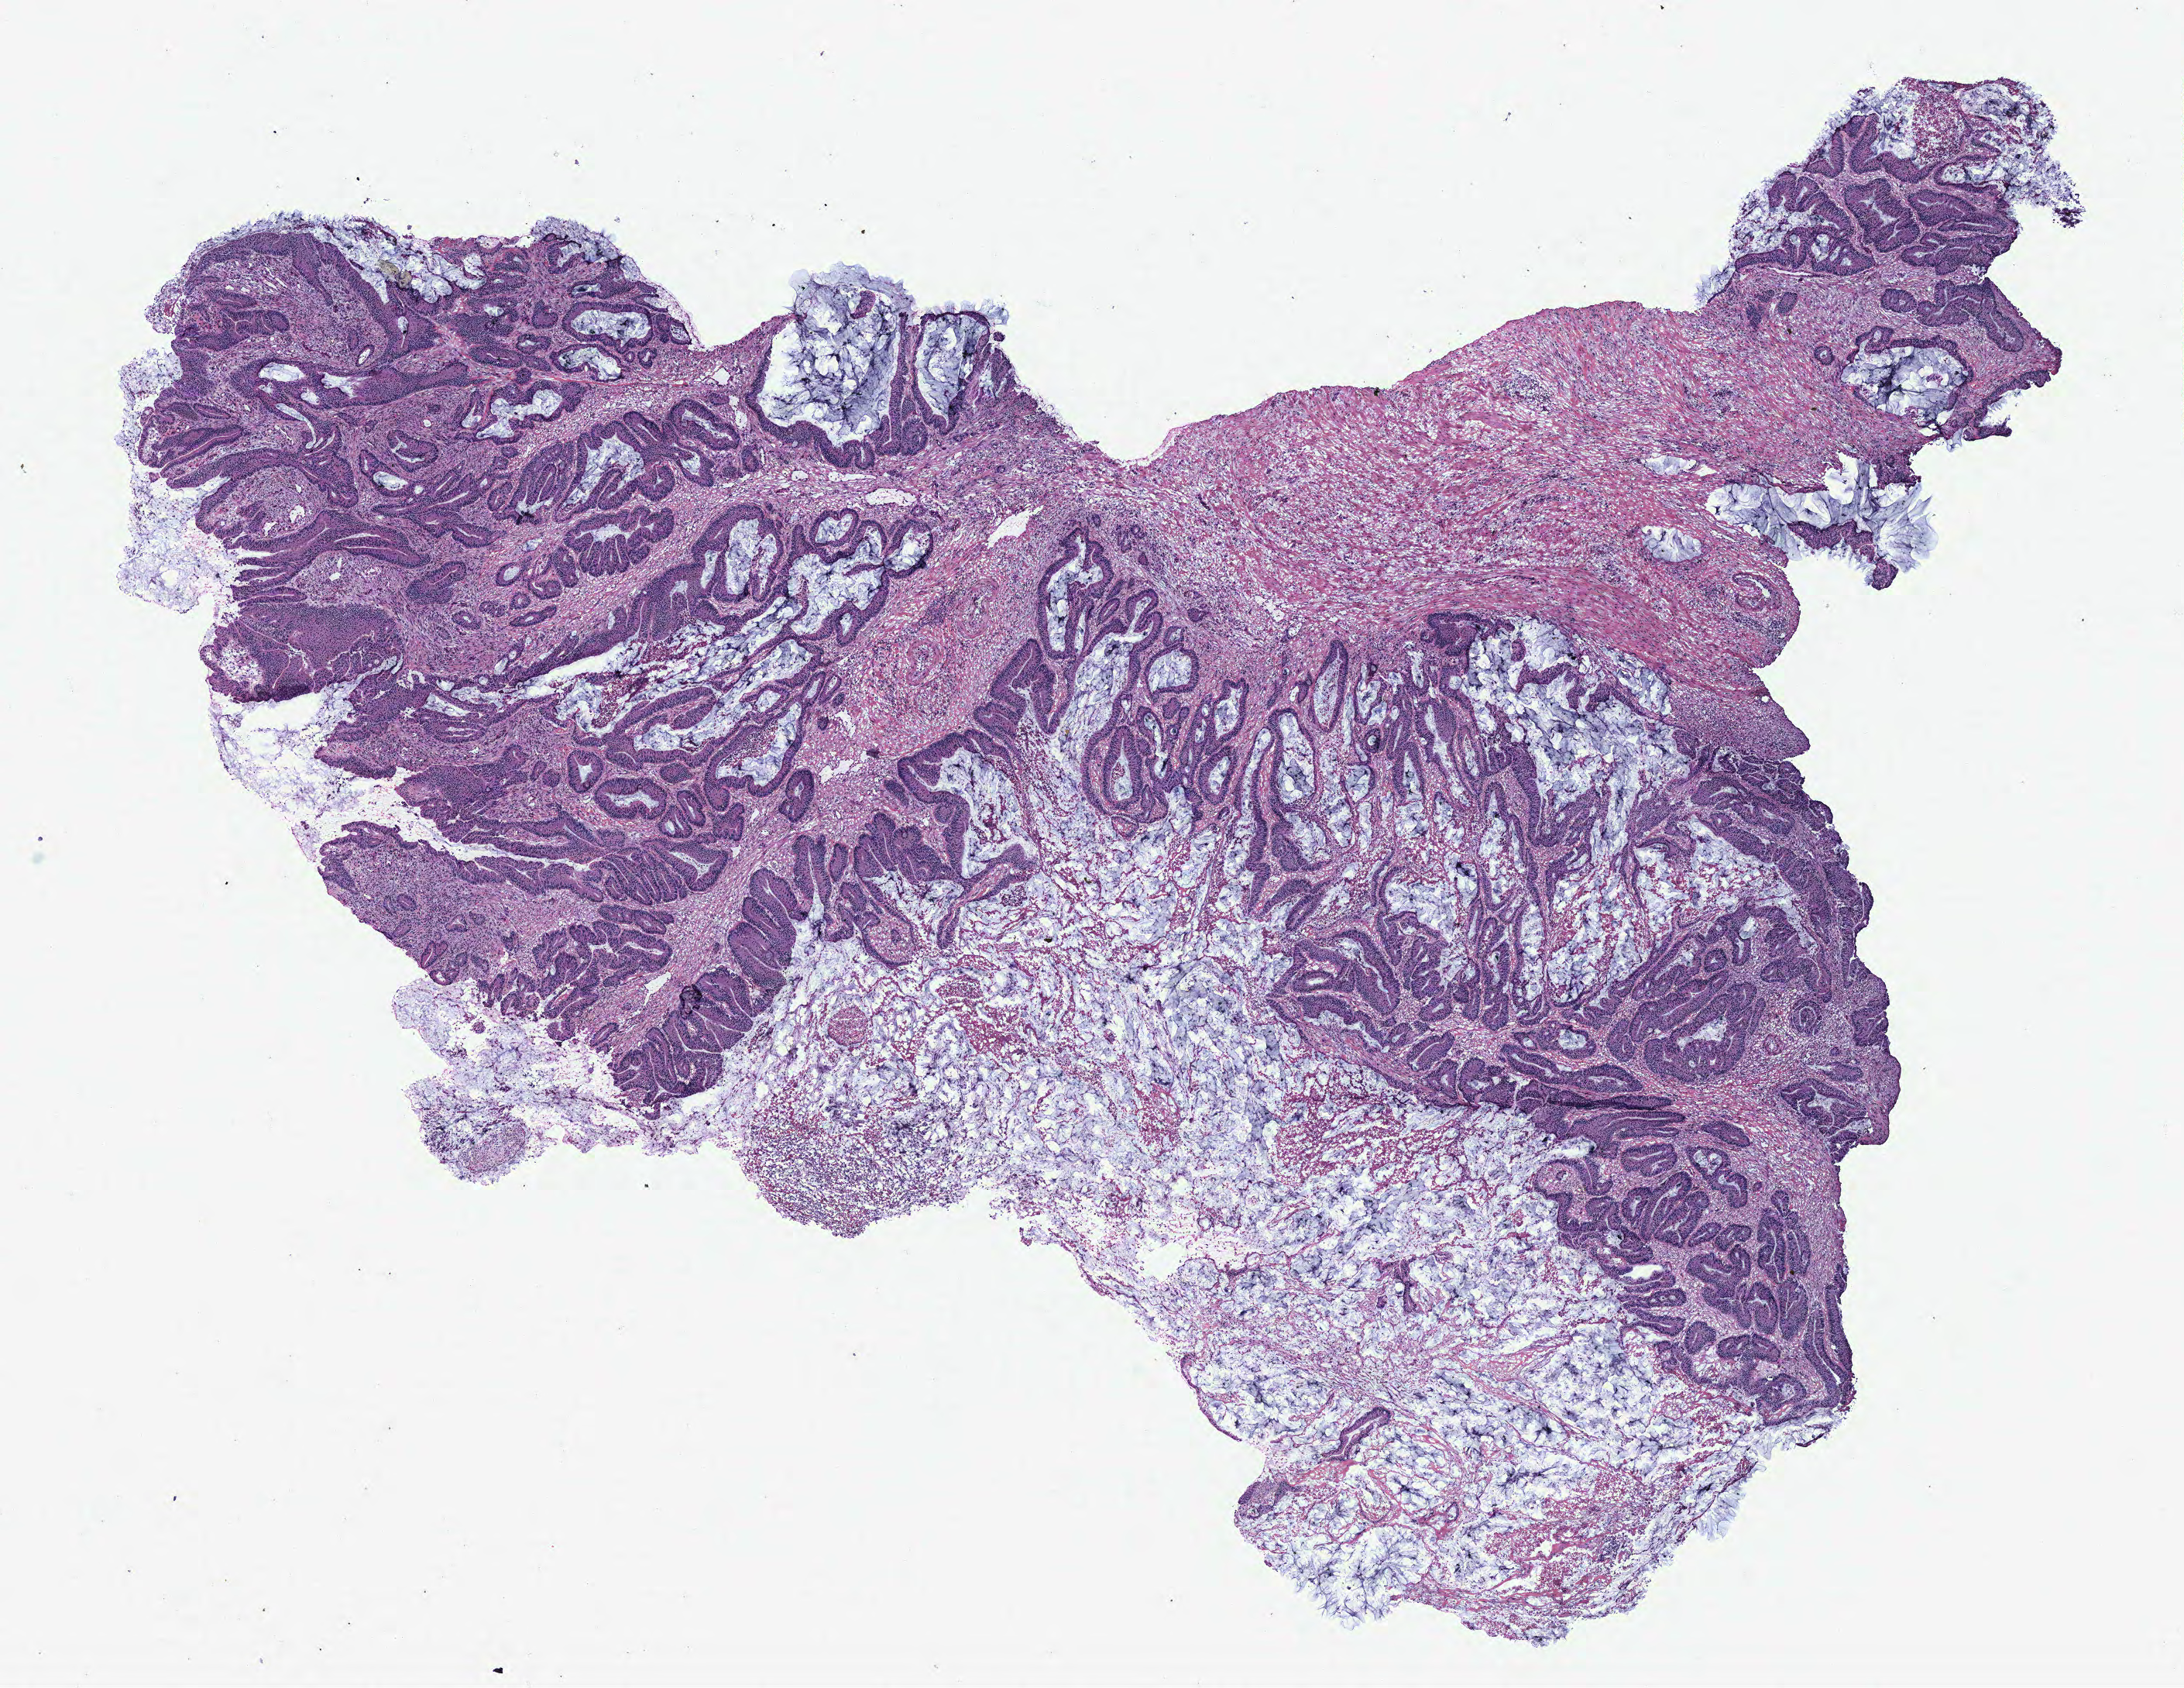
H&E whole-slide image, shown as a low-resolution overview of the whole scanned area (about 11.3 x 8.7 mm, from a 40x scan); tumour tissue sample, colon. 50-year-old male patient.
* primary tumour site (as recorded): colon
* AJCC pathologic stage: IIA
* diagnosis: Adenocarcinoma, NOS